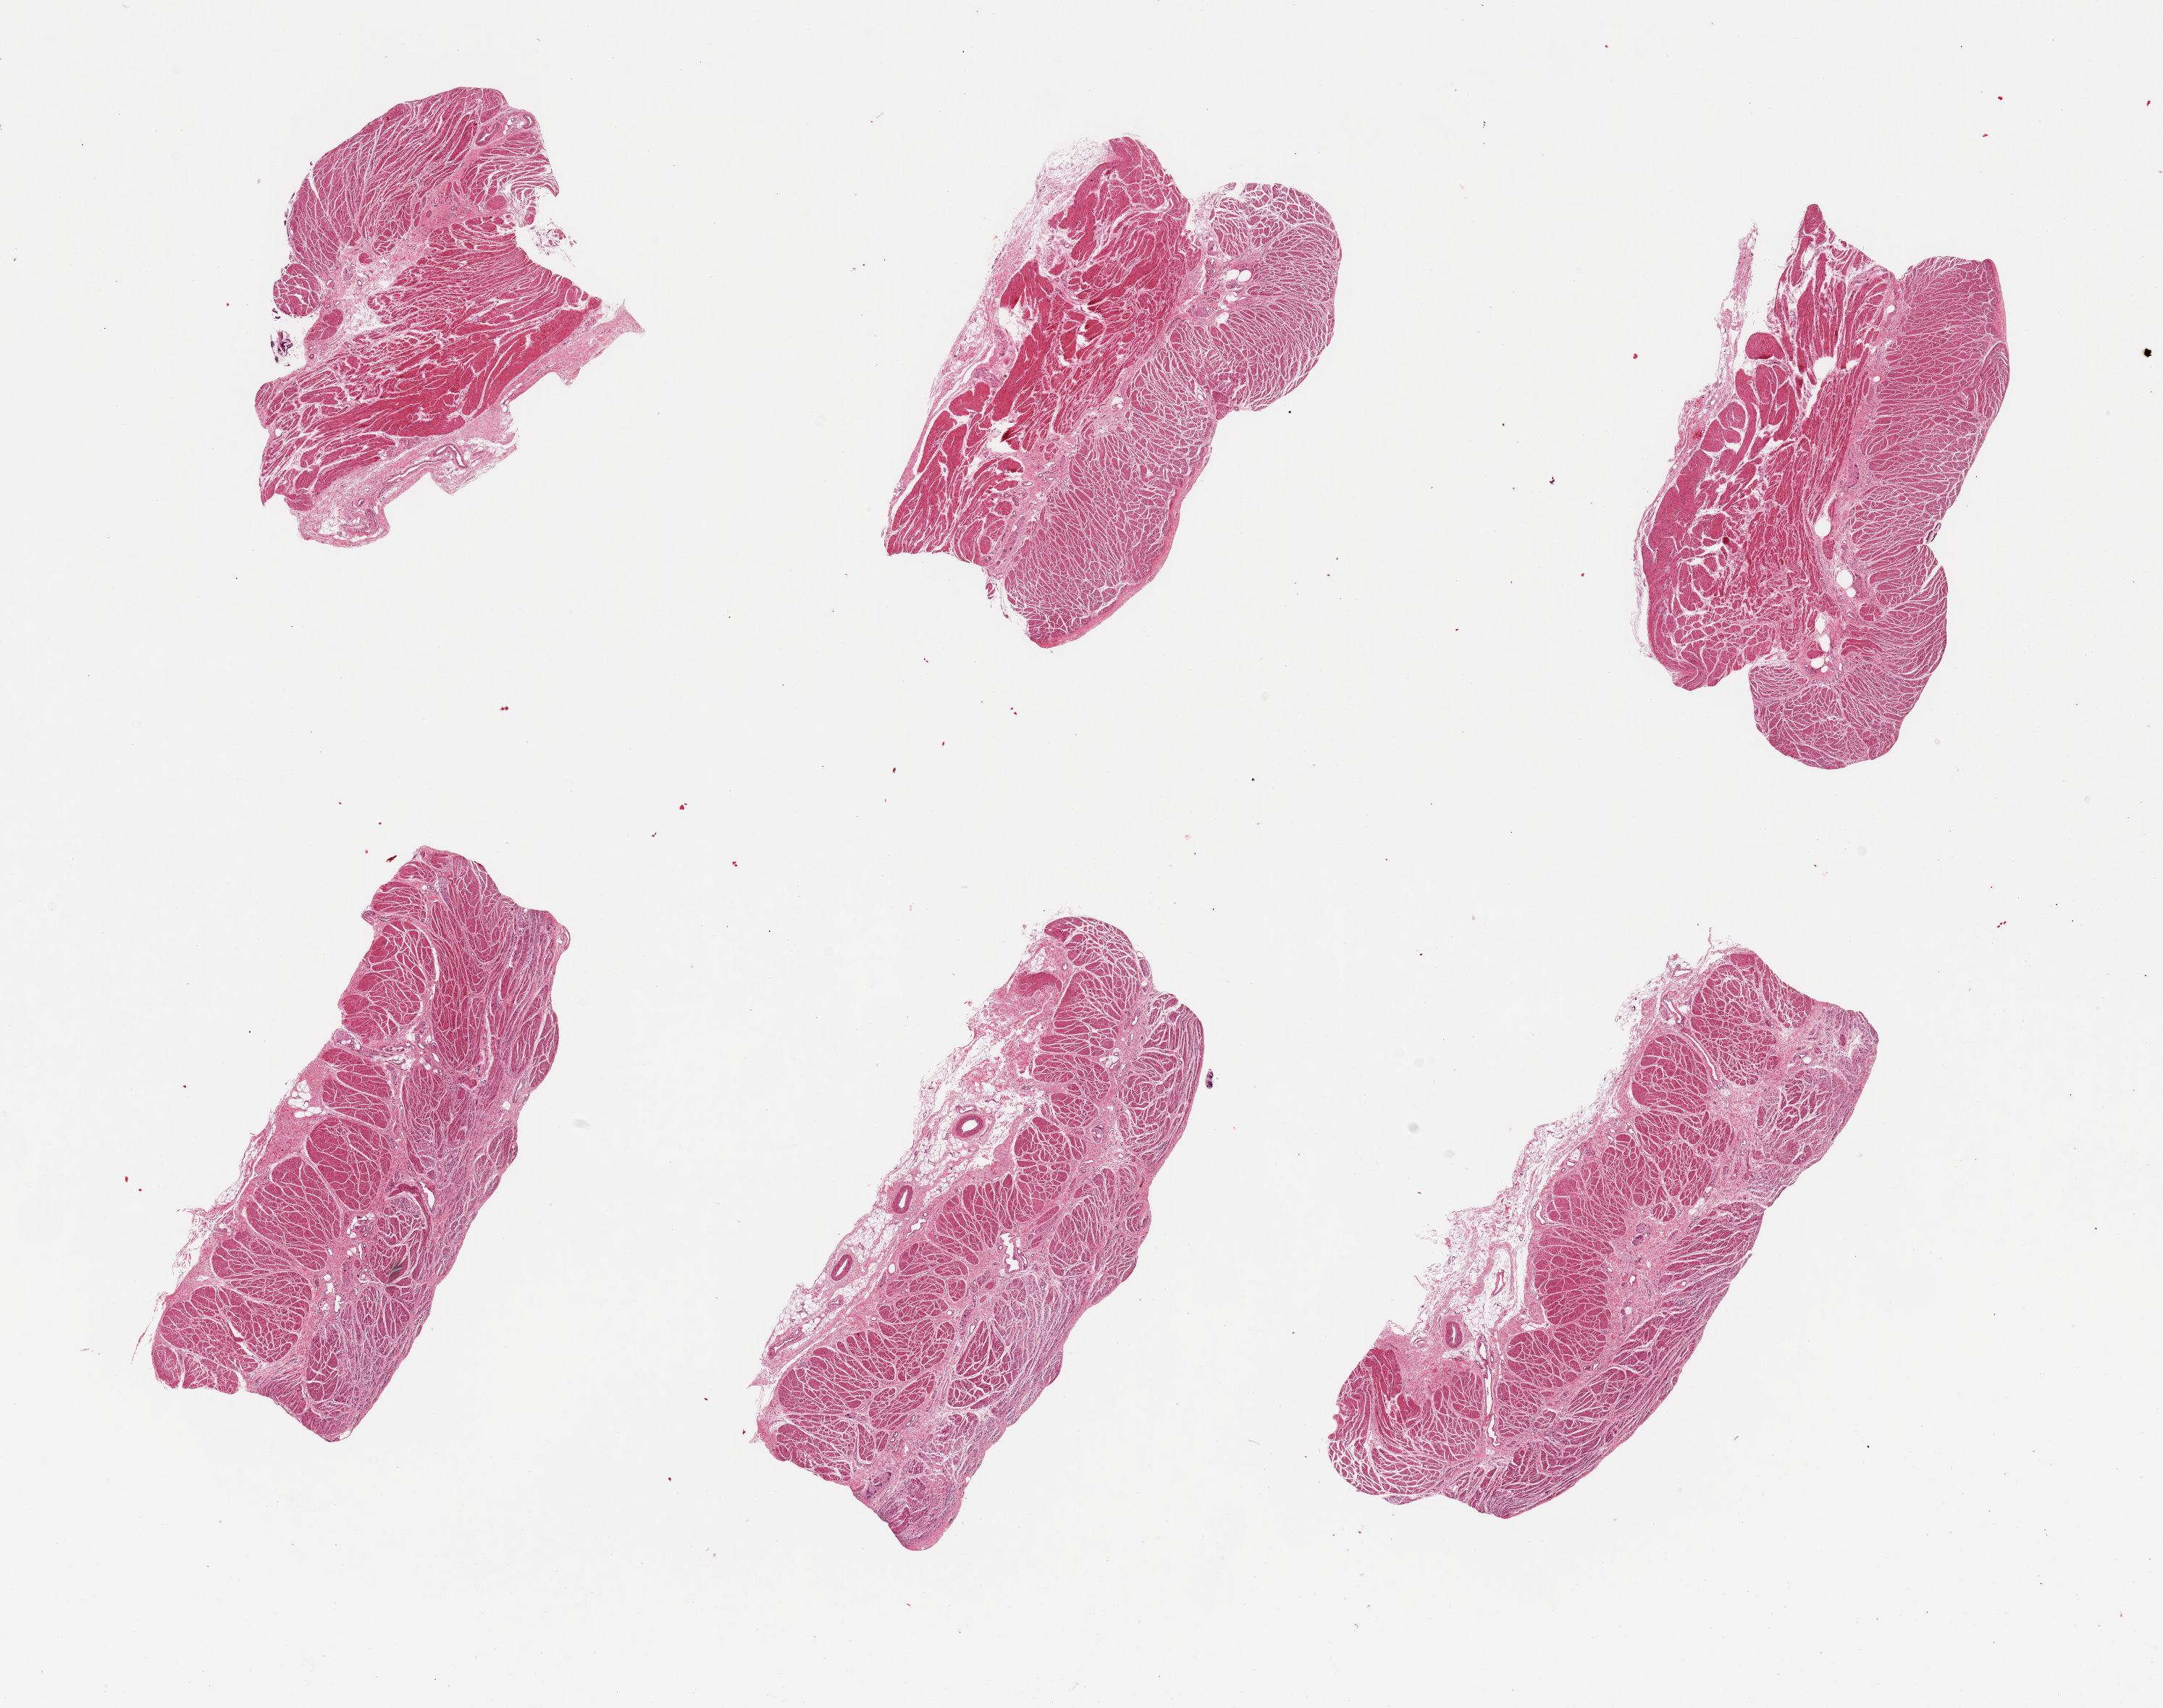
Digitized H&E-stained section, brightfield — low-resolution overview of the scanned area, about 23.6 x 18.7 mm (acquisition: 20x scan); PAXgene-fixed paraffin-embedded (PFPE) section; target tissue: gastroesophageal junction; tissue donor sample. Male donor.
Review note (as recorded): 6 pieces, good specimens, well-trimmed of mucosa.